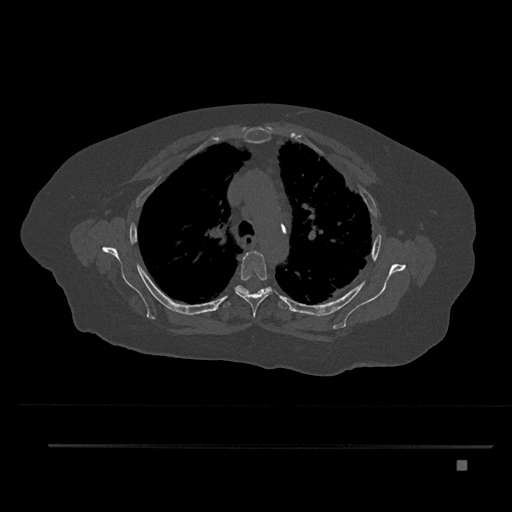
CT including the spine, one axial slice. Position 596 of 797 along the scan axis. Reconstruction kernel Br40s/3. 120 kVp. Bone window (W 1800 / L 400 HU). 0.5 mm slice thickness. 512 × 512 image matrix, field of view 437 × 437 mm. Patient: female, 76 years. Case-level facts recorded for this patient, not image findings: primary cancer: lung.
Structures marked on this image (semi-automatically segmented with operator editing):
- T3 vertebra: bounding box <244,254,247,258> (left, top, right, bottom; pixels)
- T4 vertebra: <234,251,272,318>
- T5 vertebra: <224,285,290,309>